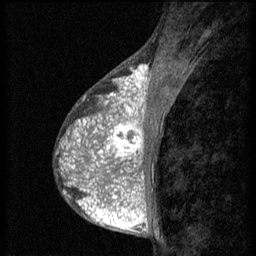
Breast MRI (dynamic contrast-enhanced), one sagittal slice. Position 26 of 60 along the scan axis. 3 images stored at this slice position (order not interpretable as contrast timing). 1.5 T. TE 4.2 ms, TR 8.2 ms. 2 mm slice thickness. 256 × 256 image matrix. Patient: female, 38 years.
Annotated regions visible in this slice (semi-automatically segmented with operator editing):
- analysis volume of interest (the breast-tissue region the enhancement analysis was run in; not a lesion): bounding box [x1, y1, x2, y2] px = [92, 112, 152, 171]
- tumour enhancement mask (voxels above the 70 % enhancement threshold inside the analysis volume of interest): [92, 112, 145, 171]